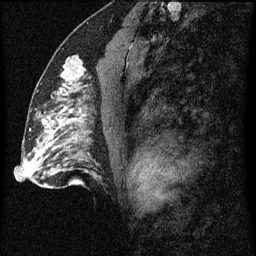
Breast MRI (dynamic contrast-enhanced), one sagittal slice; dynamic contrast-enhanced series, image 2 of 3 at this slice position (ordered by acquisition); 1.5 T; TE 4.2 ms, TR 8 ms; 2 mm slice thickness; 256 × 256 image matrix. Female patient, age 51 years.
Outlined on this slice (semi-automatic segmentation, software-assisted and operator-edited):
- analysis volume of interest (the breast-tissue region the enhancement analysis was run in; not a lesion): box from (x=55, y=54) to (x=92, y=103) px
- tumour enhancement mask (voxels above the 70 % enhancement threshold inside the analysis volume of interest): (x=58, y=68)–(x=82, y=95)